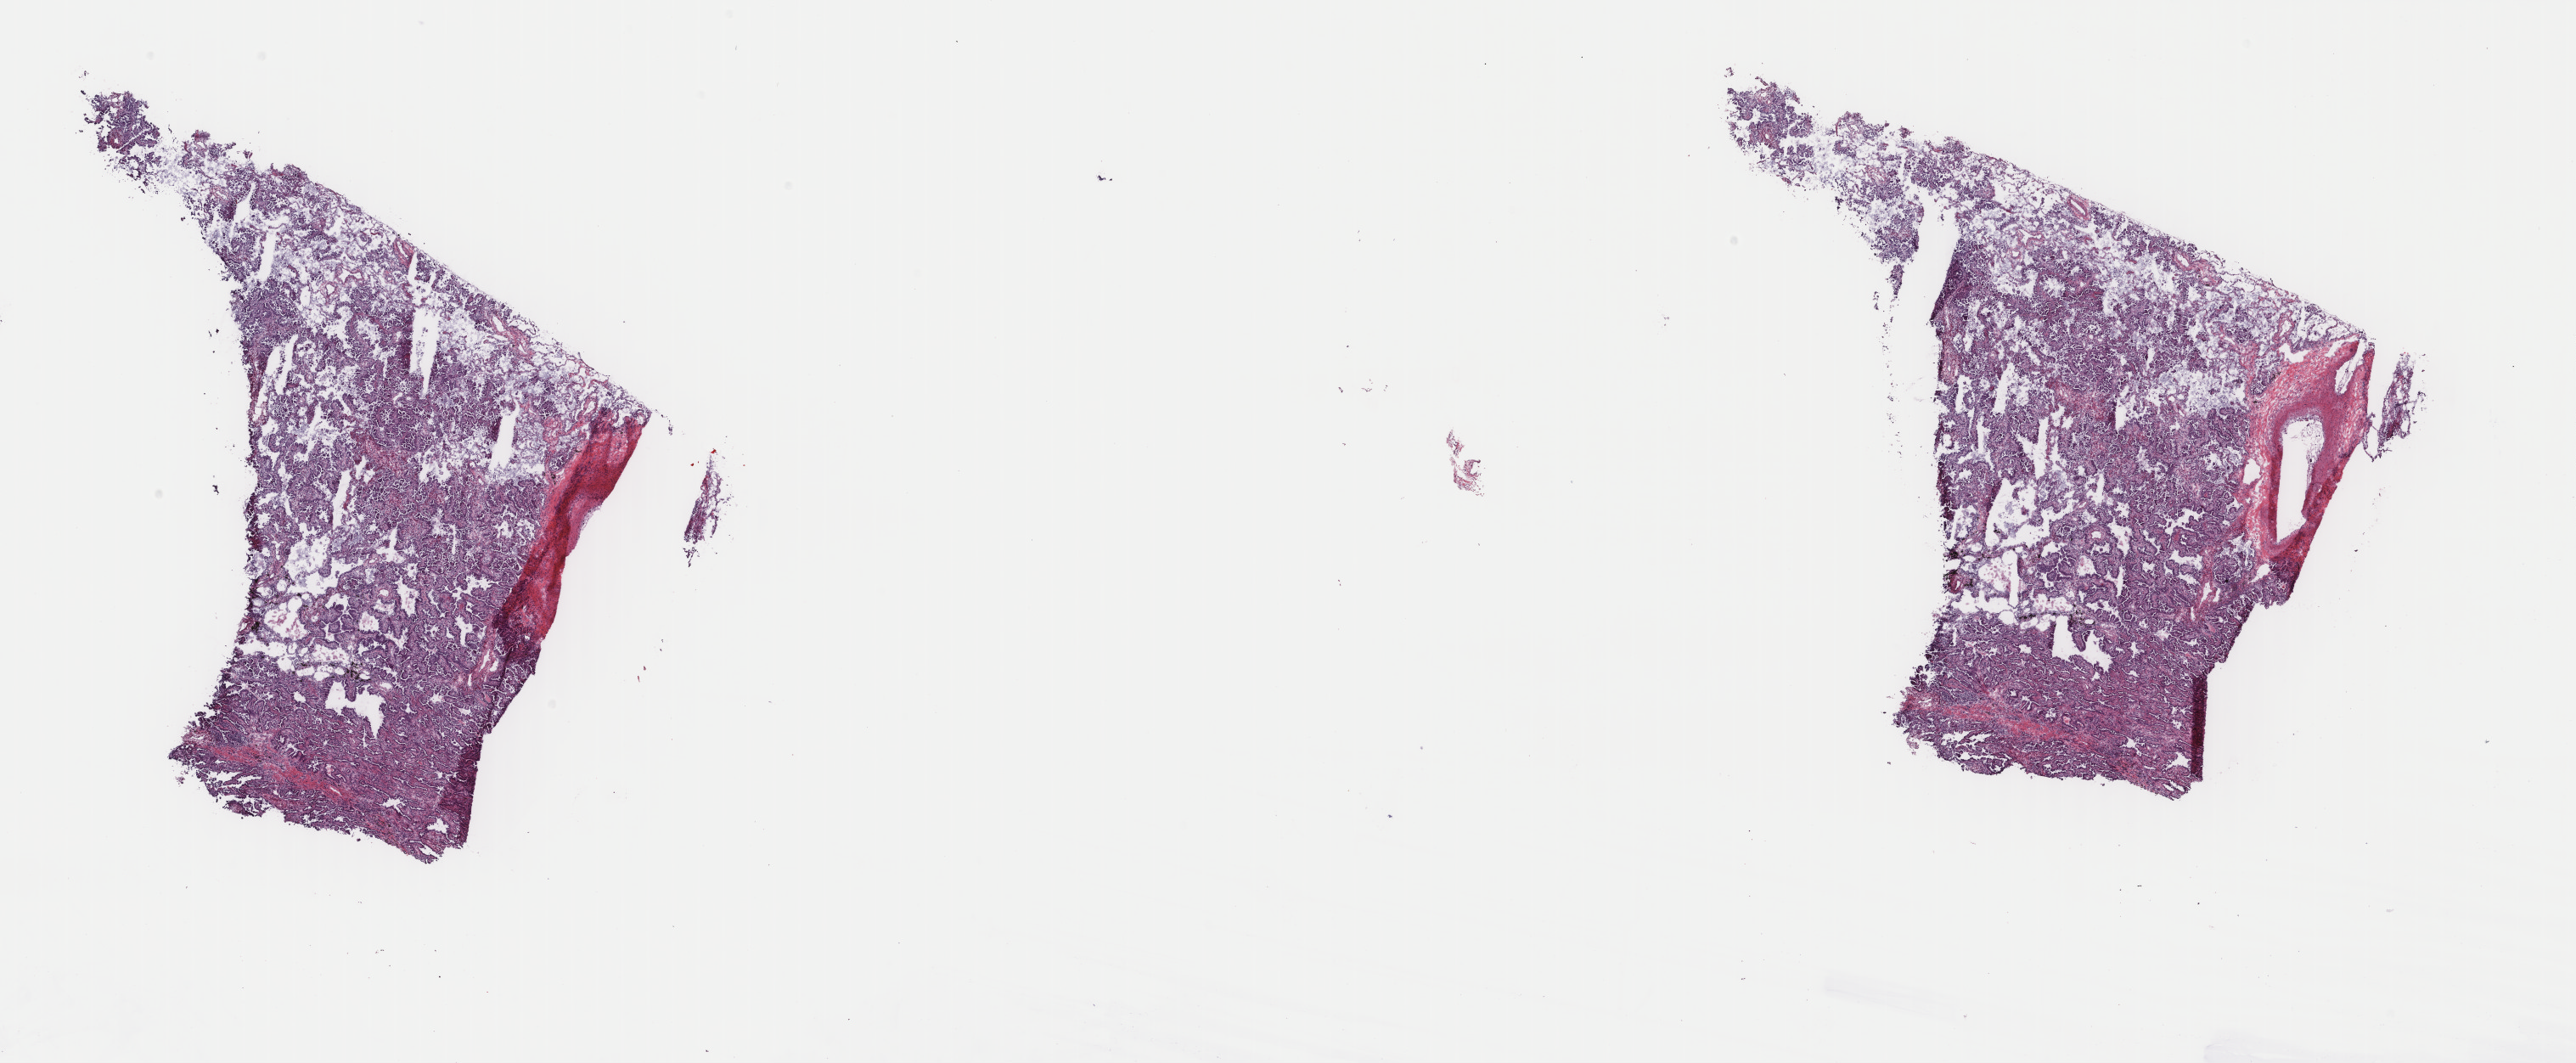
H&E whole-slide image — low-resolution overview of the scanned area, about 24.1 x 9.9 mm (from a 40x scan). Frozen section from the top of the tissue portion. Sample: primary tumour, lung. Patient: male, age at initial diagnosis 43 years. Slide review estimates, as recorded: tumour cells 75%, tumour nuclei 75%, normal cells 0%, stromal cells 25%, necrosis 0%. Infiltration values recorded for this section: lymphocyte infiltration 4%, monocyte infiltration 2%, neutrophil infiltration 3%.
Histologic diagnosis: Adenocarcinoma, NOS (upper lobe, lung). AJCC pathologic stage: IB (6th edition).